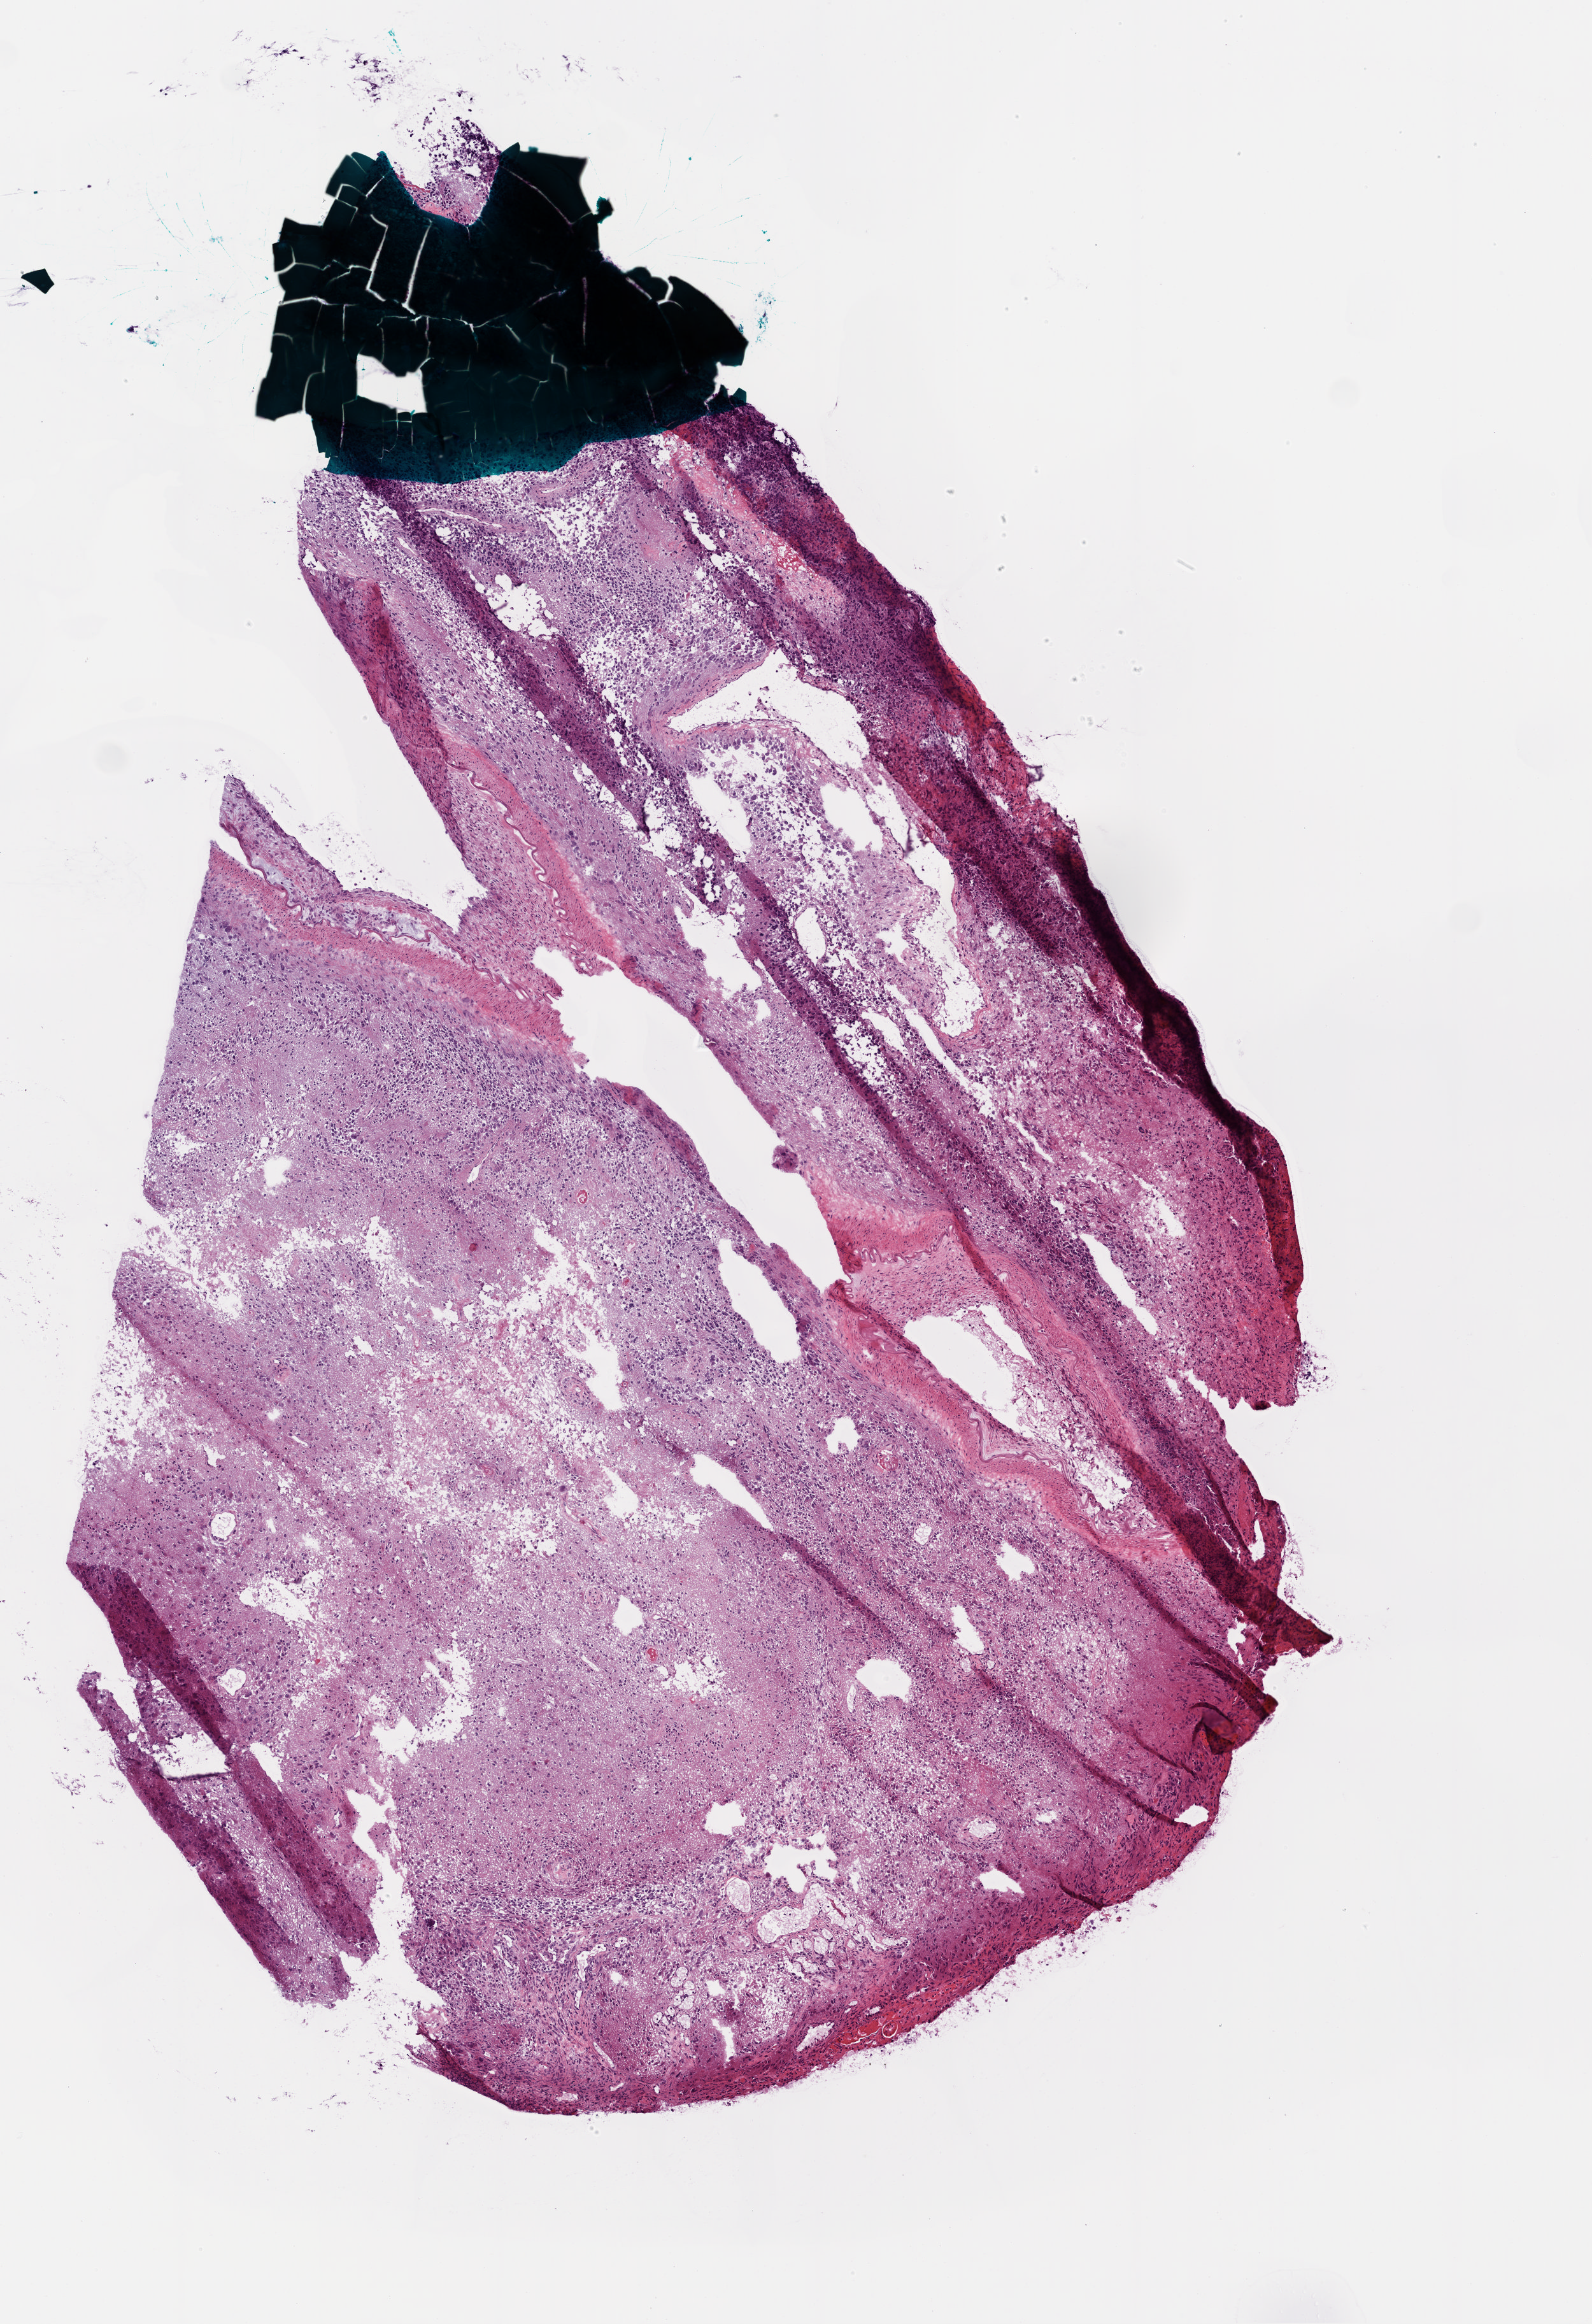
Digitized H&E-stained tissue section (whole slide) — a low-resolution overview of the entire scanned area, about 5.0 x 7.3 mm (from a 20x scan); frozen section from the bottom of the tissue portion; primary tumour sample from the brain. Female patient; age at initial diagnosis 77 years. Slide review estimates, as recorded: tumour cells 30%, tumour nuclei 100%.
Histologic diagnosis: Glioblastoma.